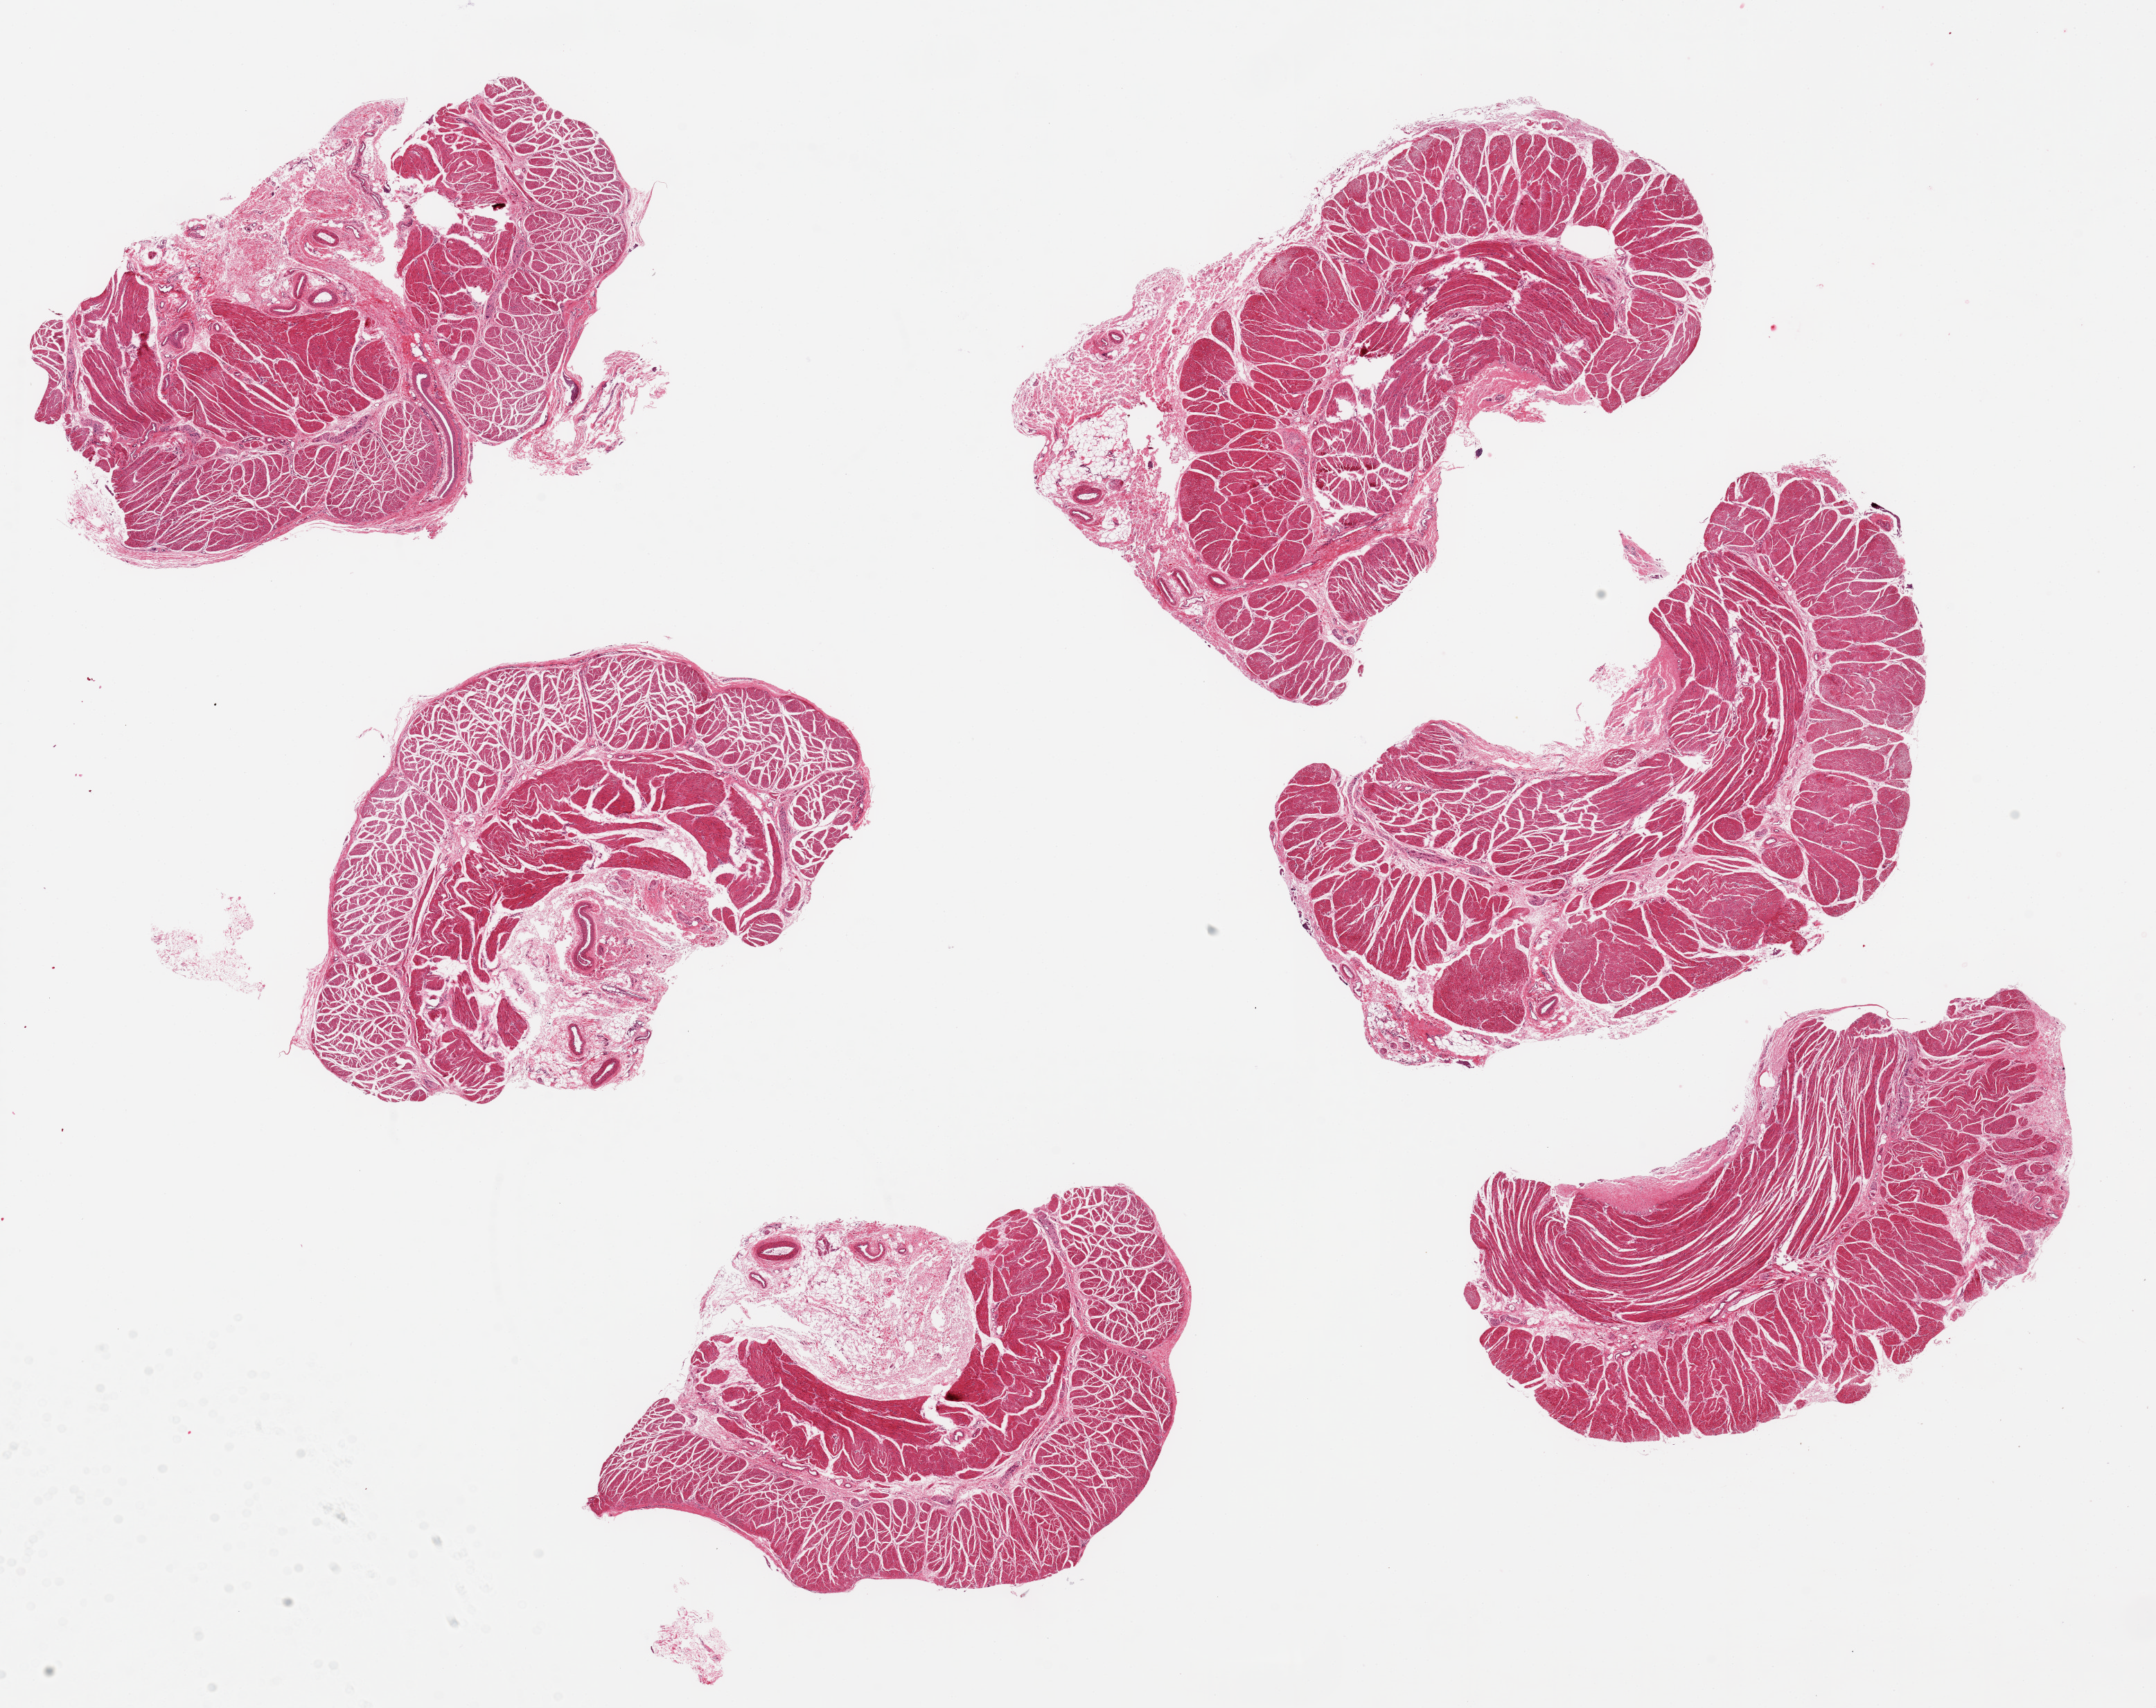
Digitized H&E-stained section, brightfield — a low-resolution overview of the entire scanned area, about 24.6 x 19.5 mm (acquisition: 20x scan); PAXgene-fixed paraffin-embedded (PFPE) section; target tissue: esophageal muscle; tissue donor sample.
• reviewer comment on this tissue sample: 6 pieces with mucosa, ~4 x 7mm, mucosa ~25% of thickness